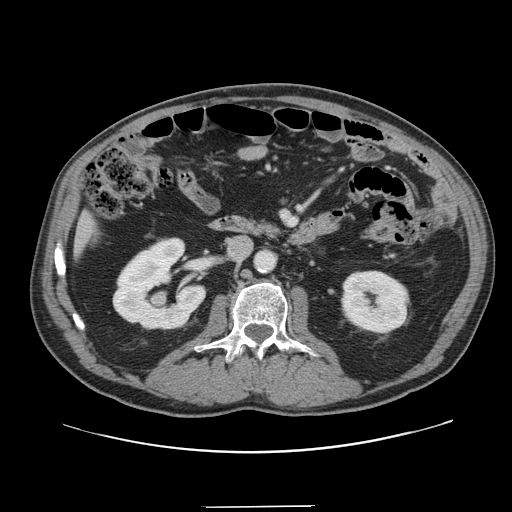
Contrast-enhanced abdominal CT, one axial slice; slice 52 of 139 in the series (ordered by position); 120 kVp; soft-tissue window (W 400 / L 40 HU); 2.5 mm slice thickness; 512 × 512 image matrix, field of view 397 × 397 mm. Male patient, age 64 years. From the clinical record (not read from this slice): diagnosis: colorectal cancer liver metastases, imaged before liver resection; multiple liver metastases: yes; largest metastasis: 3.5 cm; disease in both lobes: yes.
Structures marked on this image (outlined manually by an expert reader):
- liver: box from (x=77, y=217) to (x=92, y=253) px
- planned liver remnant (the part of the liver to remain after resection): (x=77, y=218)–(x=91, y=252)